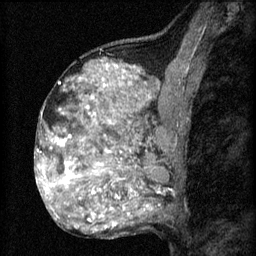
Breast MRI (dynamic contrast-enhanced), one sagittal slice; 3 images stored at this slice position (order not interpretable as contrast timing); 1.5 T; TE 4.2 ms, TR 8.2 ms; 2 mm slice thickness; 256 × 256 image matrix. Patient: female, 48 years.
Annotated regions visible in this slice (semi-automatically segmented with operator editing):
- analysis volume of interest (the breast-tissue region the enhancement analysis was run in; not a lesion): bounding box <61,138,153,201> (left, top, right, bottom; pixels)
- tumour enhancement mask (voxels above the 70 % enhancement threshold inside the analysis volume of interest): <61,138,136,199>